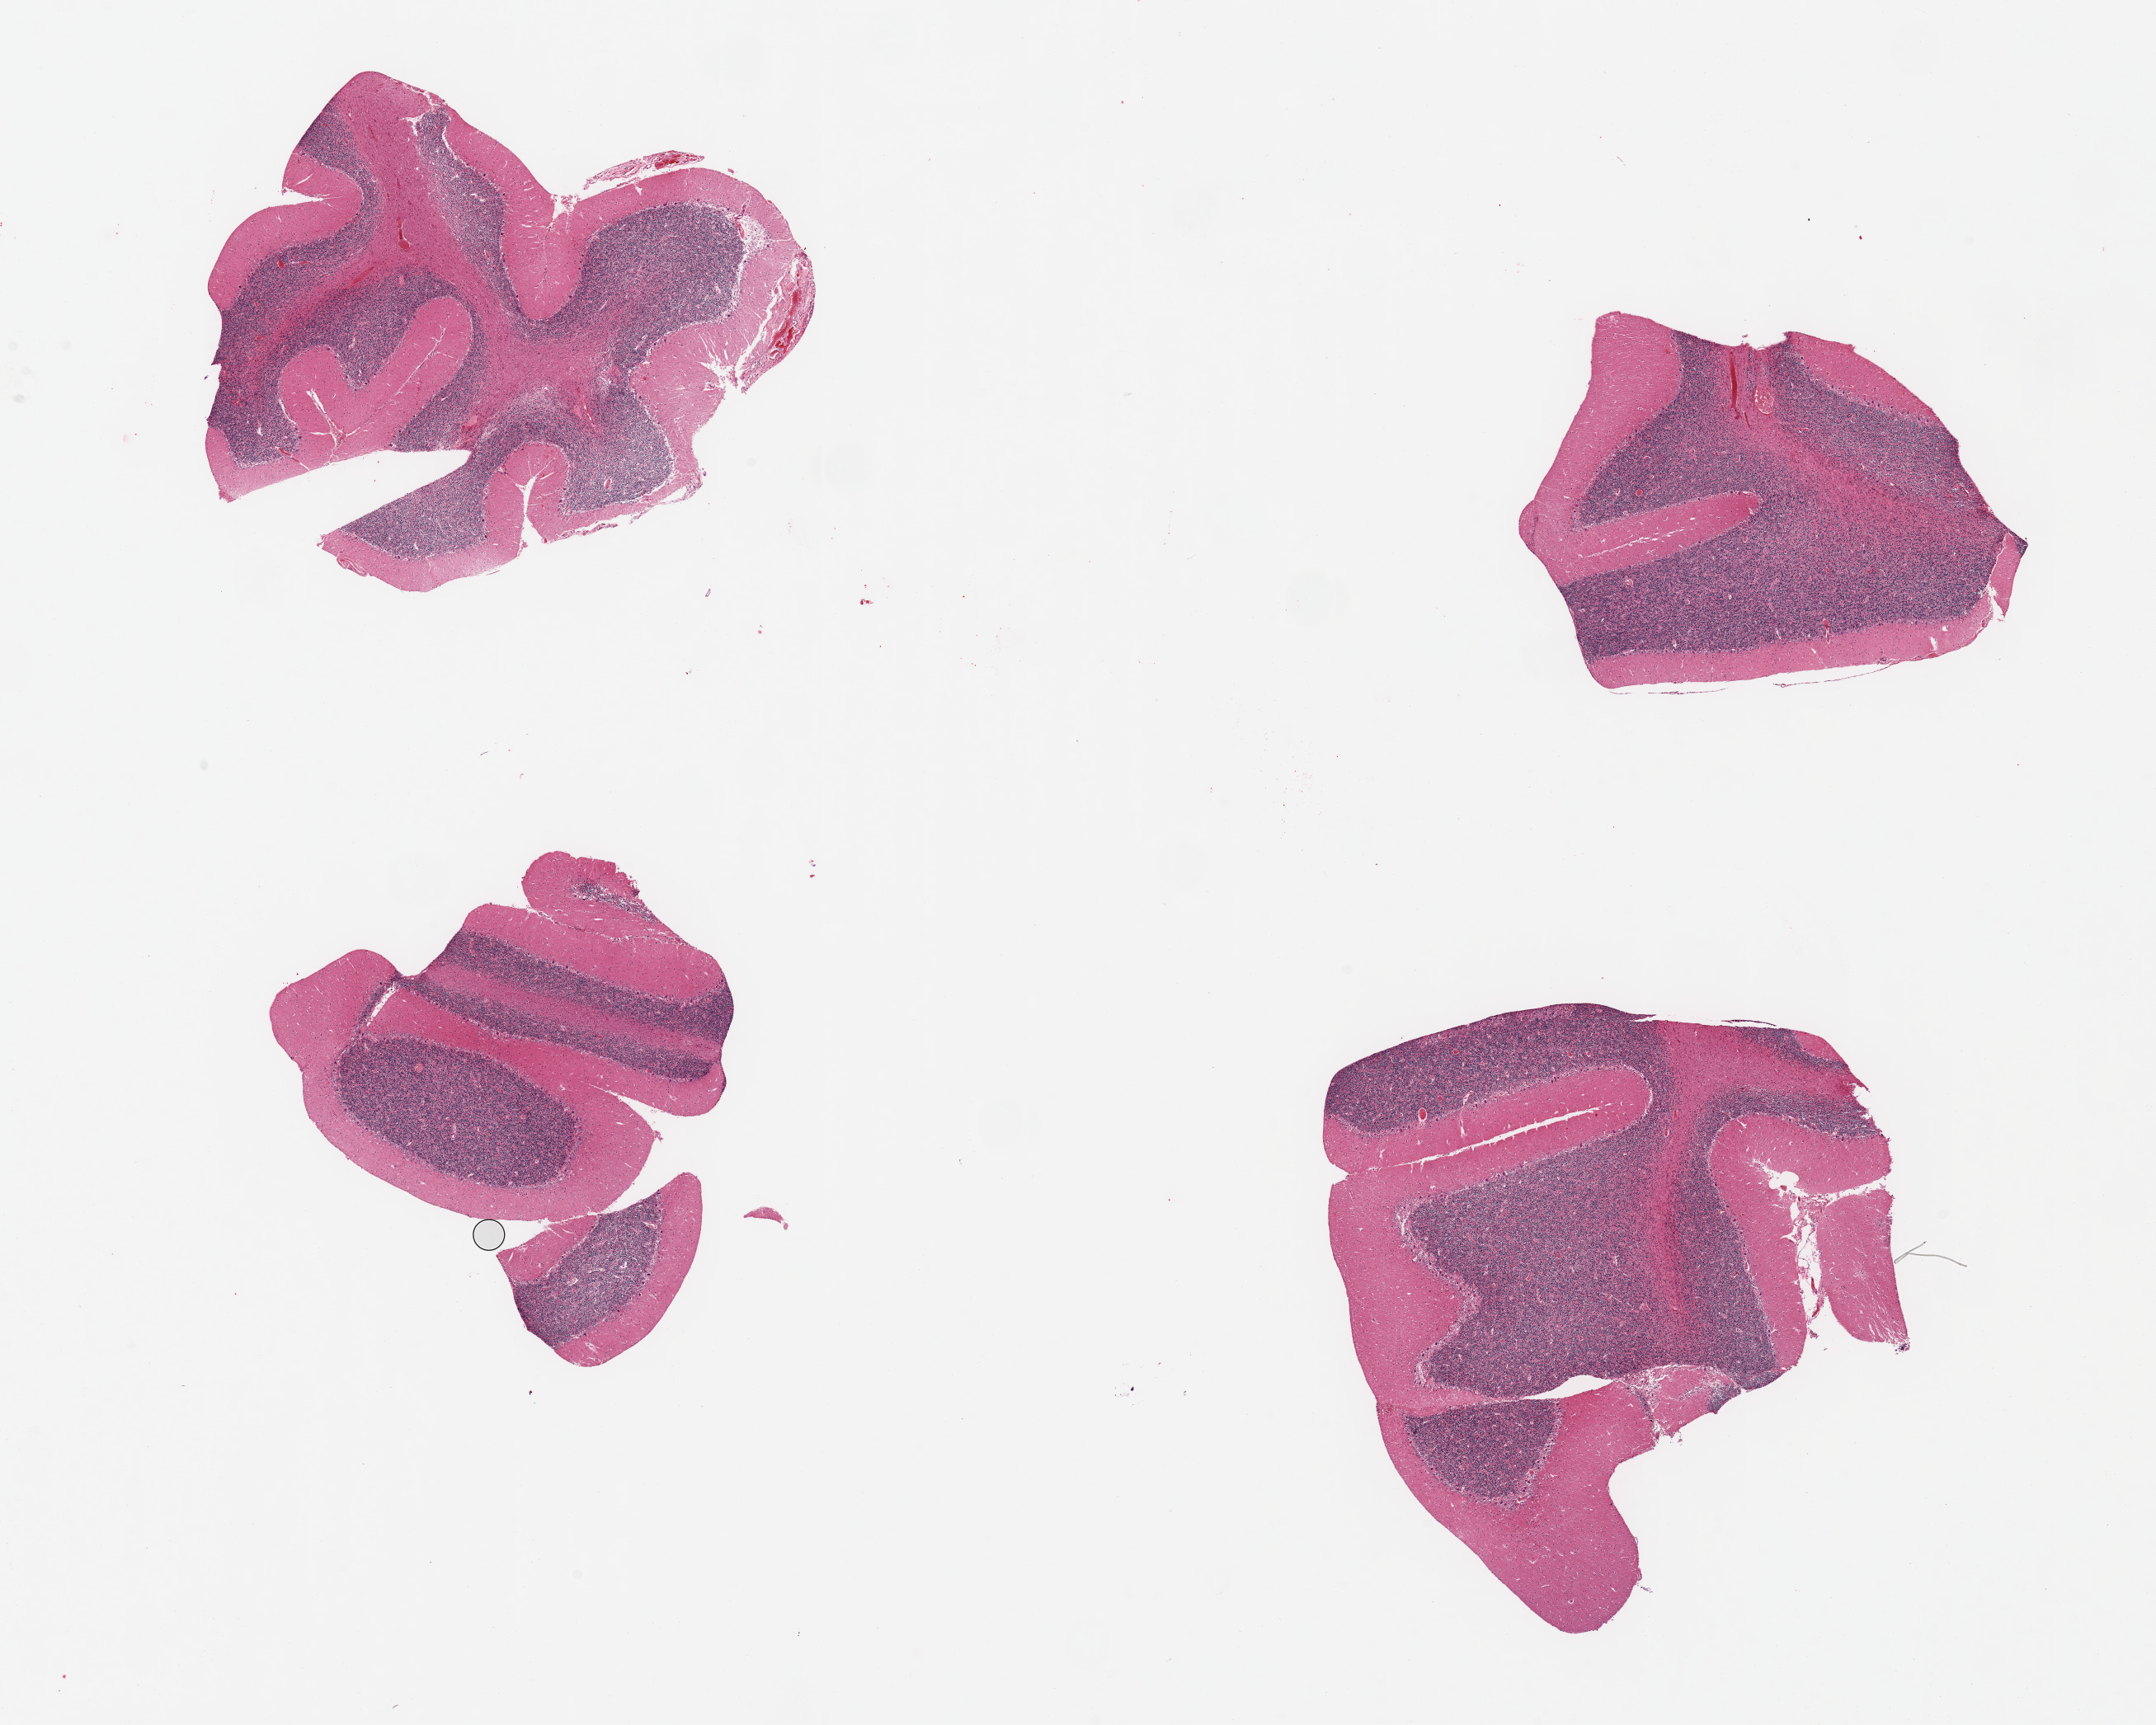
Digitized hematoxylin and eosin (H&E)-stained section — a low-resolution overview of the entire scanned area, about 20.7 x 16.5 mm; PAXgene-fixed, paraffin-embedded tissue; target tissue: cerebellum; tissue donor sample.
• pathologist's review note for this sample: 4 pieces